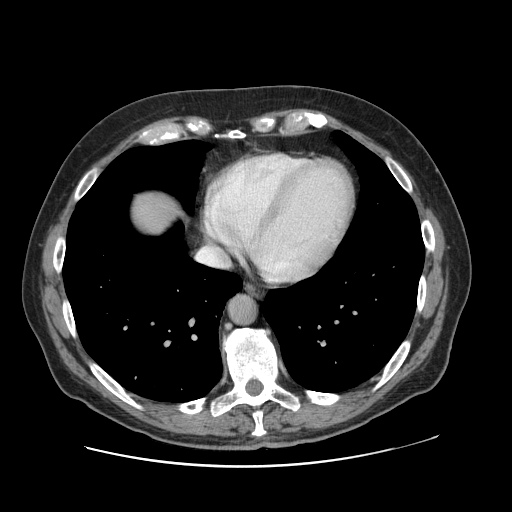
Contrast-enhanced abdominal CT, one axial slice; 120 kVp; soft-tissue window (W 400 / L 40 HU); 2.5 mm slice thickness; 512 × 512 image matrix, field of view 402 × 402 mm. Male patient, age 71 years. Case-level facts recorded for this patient, not image findings: diagnosis: colorectal cancer liver metastases, imaged before liver resection.
Annotated regions visible in this slice (manually delineated by an expert):
- liver: bounding box <127,189,185,236> (left, top, right, bottom; pixels)
- planned liver remnant (the part of the liver to remain after resection): <128,188,182,236>